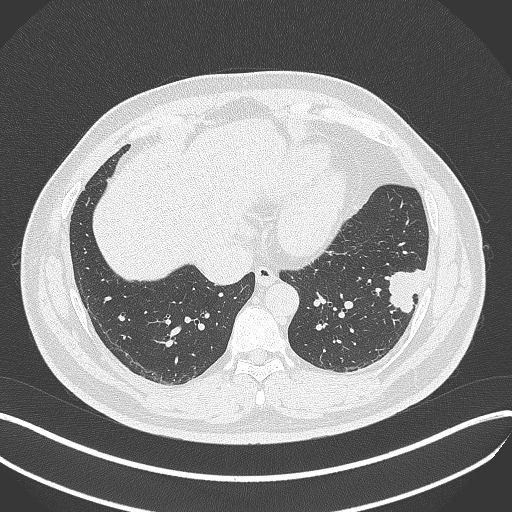
Chest CT, one axial slice; slice 132 of 429 in the series (ordered by position); lung window (W 1500 / L -600 HU); 1 mm slice thickness; 512 × 512 image matrix, field of view 400 × 400 mm. Male patient, age 39 years. Case-level facts recorded for this patient, not image findings: clinical TNM (as recorded): T2a N0 M0.
Outlined on this slice (bounding box drawn by a radiologist):
- lung tumour (recorded histology: adenocarcinoma): box from (x=379, y=264) to (x=432, y=316) px